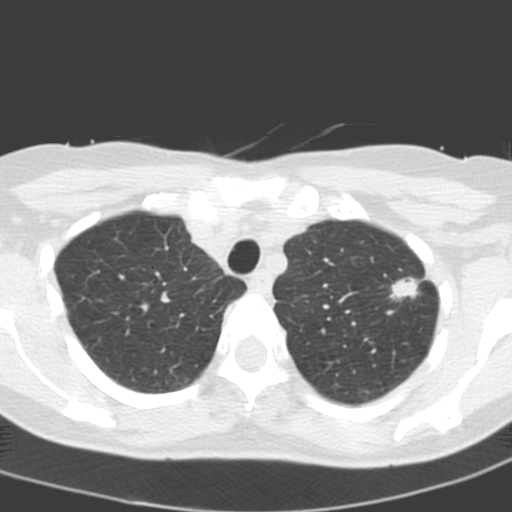
Low-dose screening chest CT, axial slice, baseline annual screen, lung window (W 1500 / L -600 HU), 3.2 mm slice thickness, slice 36 of 193 in the series. Female participant, aged 58 years at enrolment.
• Lesion marked by an expert reader, bounding box <379,267,428,316> (left, top, right, bottom; pixels).
• The exam's reader record, not a measurement of the box and not confirmed to be the same lesion: non-calcified nodule or mass ≥4 mm, left upper lobe, 14 × 10 mm, spiculated (stellate) margins, soft tissue attenuation.
• Official screen result: positive, change unspecified: nodule(s) >= 4 mm or enlarging nodule(s), mass(es), or other non-specific abnormalities suspicious for lung cancer.